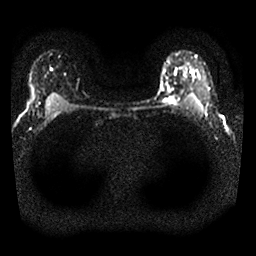
Breast MRI, one axial slice; slice 22 of 25 in the series (ordered by position); diffusion-weighted series; image 2 of 4 stored at this slice position (different b-values; order by instance number); 1.5 T; 256 × 256 image matrix, field of view 310 × 310 mm. Female patient.
Annotated regions visible in this slice (manually delineated by an expert):
- tumour on diffusion-weighted imaging: bounding box [x1, y1, x2, y2] px = [170, 96, 173, 100]